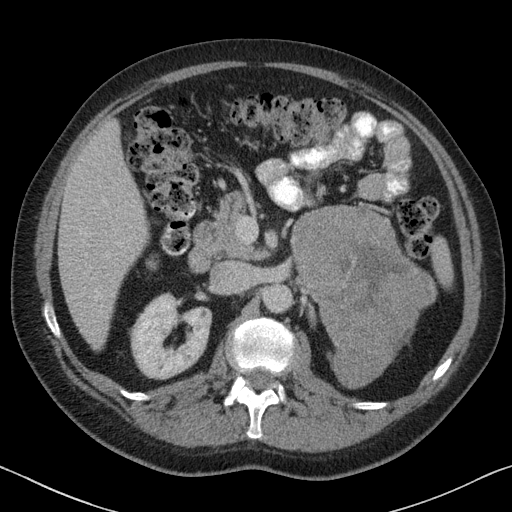
Contrast-enhanced abdominal CT, one axial slice. Slice 42 of 88 in the series (ordered by position). Intravenous contrast given. Soft-tissue window (W 400 / L 40 HU). 3 mm slice thickness. 512 × 512 image matrix. Male patient, age 51 years. Case-level facts recorded for this patient, not image findings: diagnosis: adrenocortical carcinoma; tumour side: left adrenal; tumour size at pathology: 16.5 cm; Ki-67 index: 30 %; stage (as recorded): 2.
Annotated regions visible in this slice (semi-automatic segmentation, software-assisted and operator-edited):
- mass: bounding box <292,206,434,388> (left, top, right, bottom; pixels)